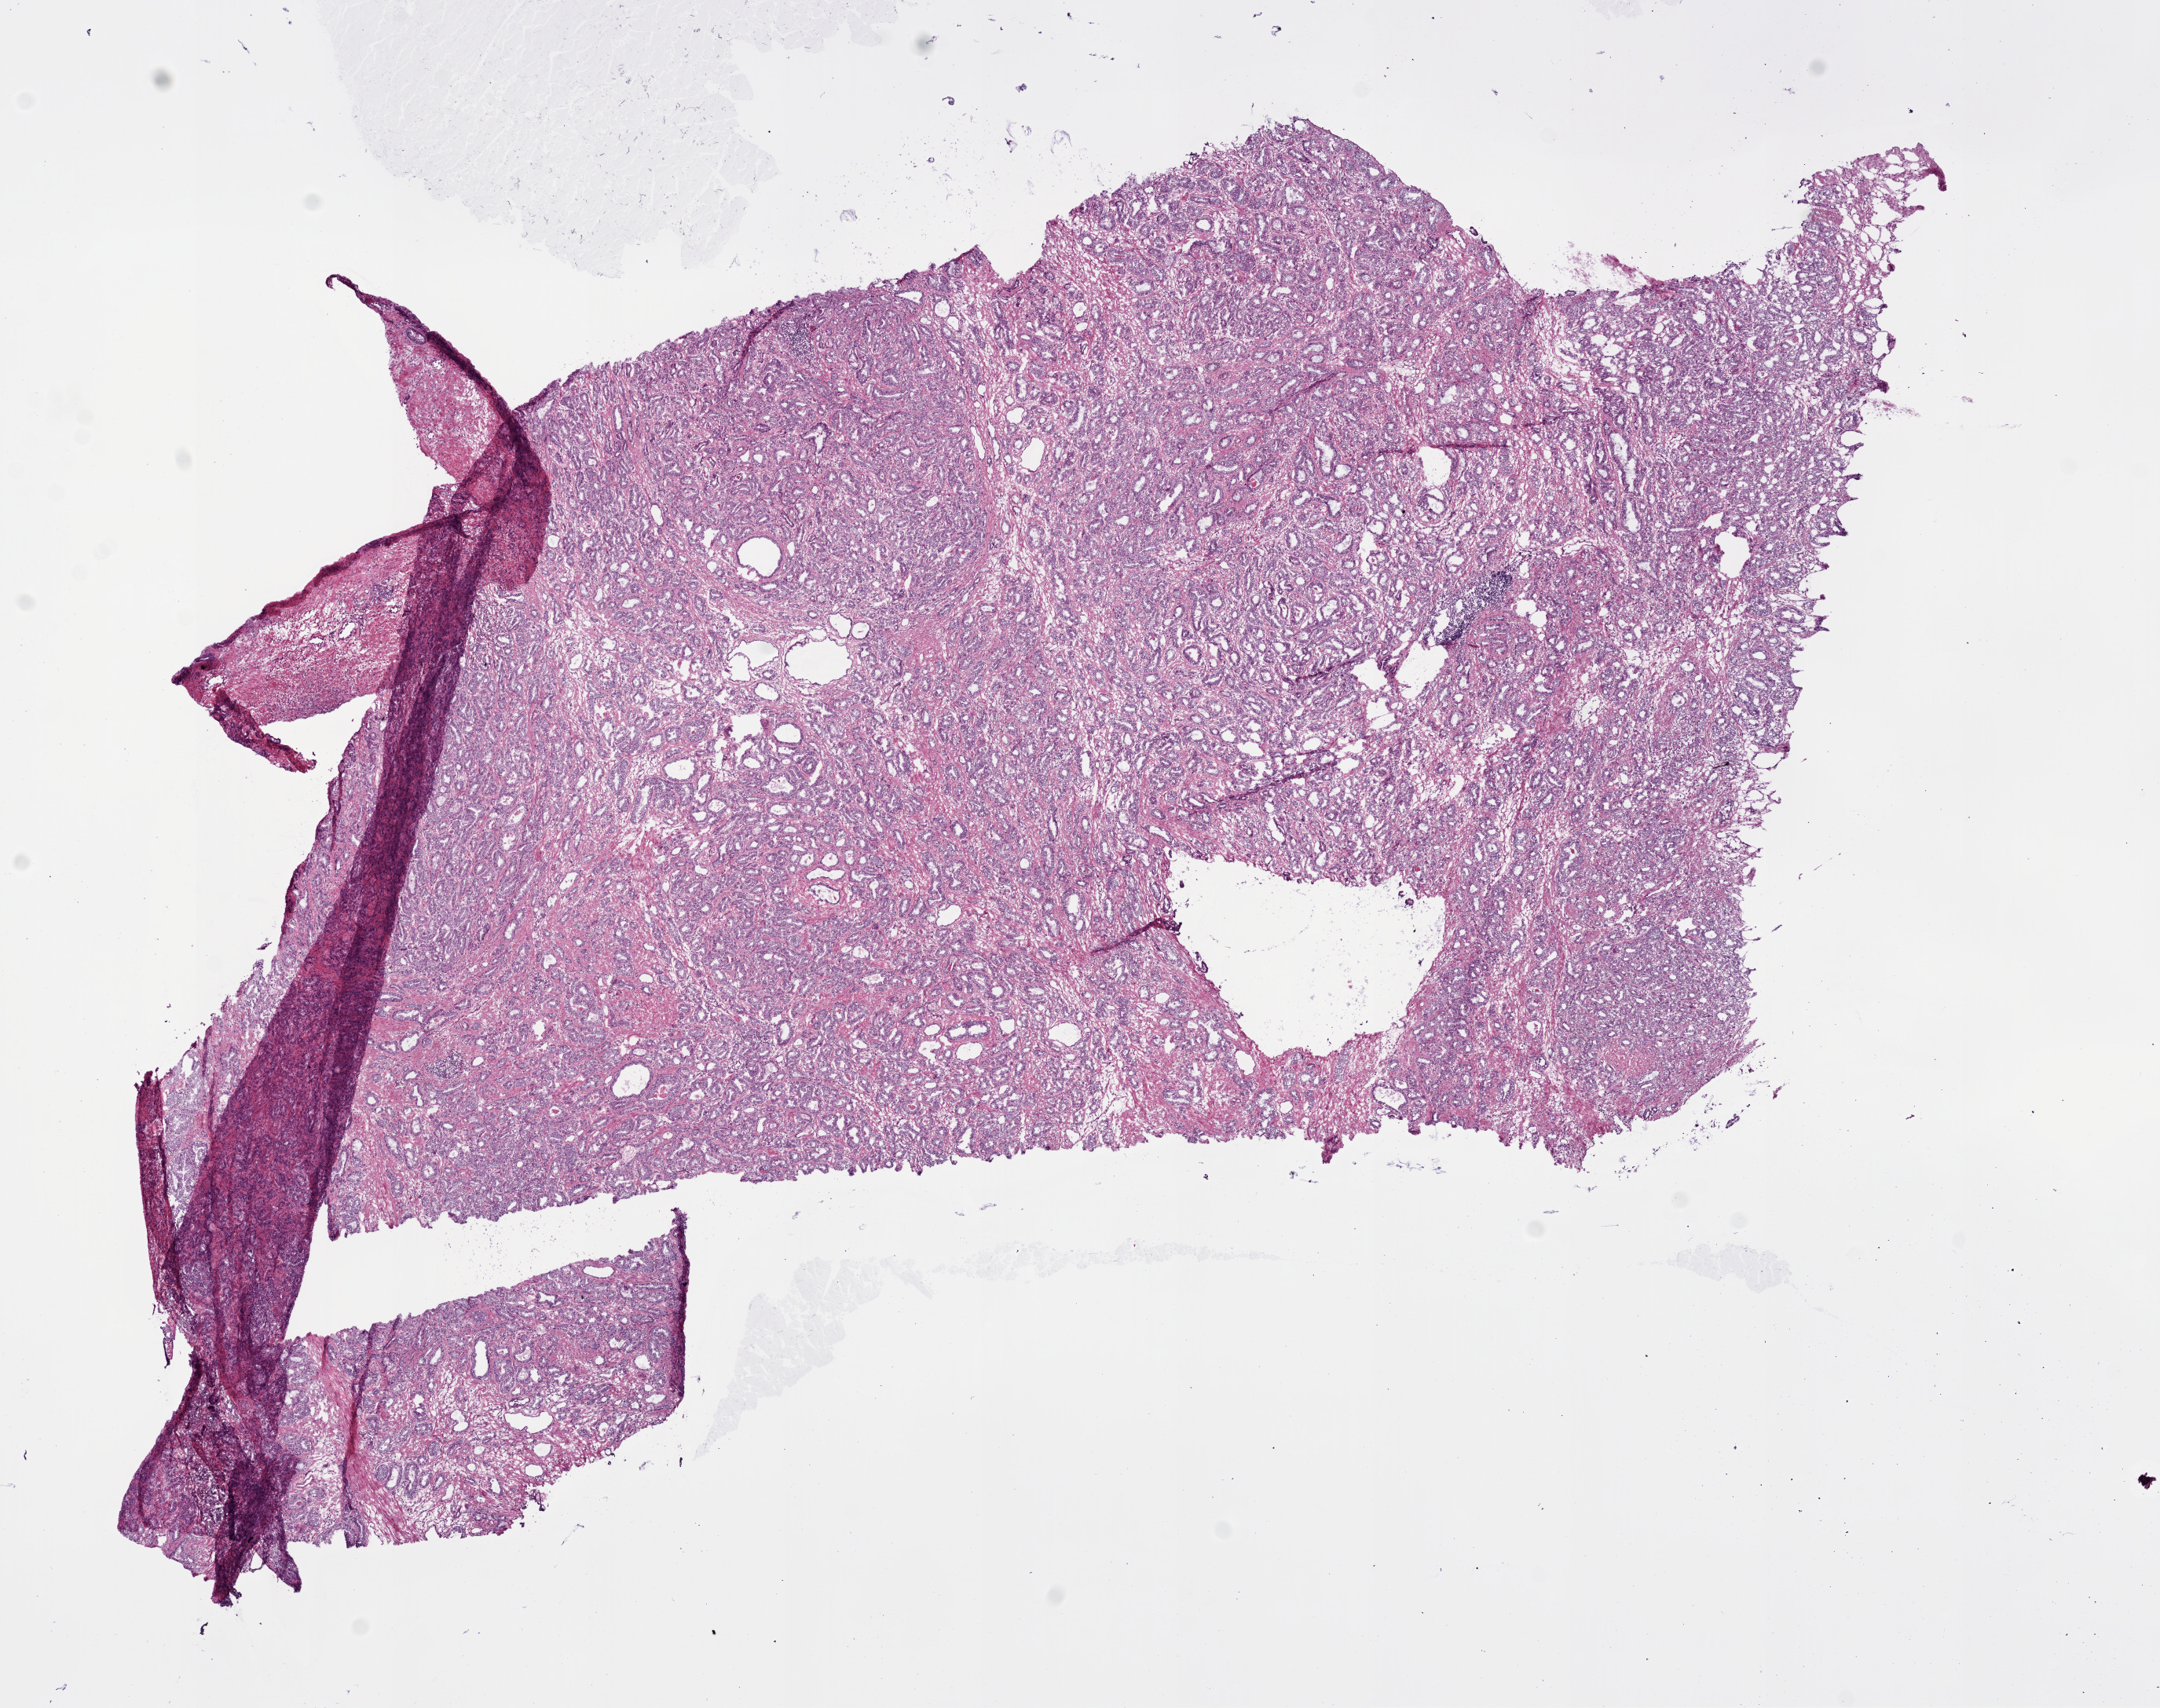
Digitized H&E-stained tissue section (whole slide) — a low-resolution overview of the entire scanned area, about 11.0 x 8.7 mm; frozen section from the bottom of the tissue portion; sample: primary tumour, prostate. Male patient; age at initial diagnosis 55 years. Gleason score: 6 (3+3). Slide review estimates, as recorded: tumour cells 75%, tumour nuclei 80%, normal cells 10%, stromal cells 15%, necrosis 0%. Infiltration values recorded for this section: lymphocyte infiltration 5%, monocyte infiltration 0%, neutrophil infiltration 0%.
* laterality: bilateral
* lymph nodes positive (case pathology): 0 of 4 examined
* histologic diagnosis: Acinar cell carcinoma (prostate gland)